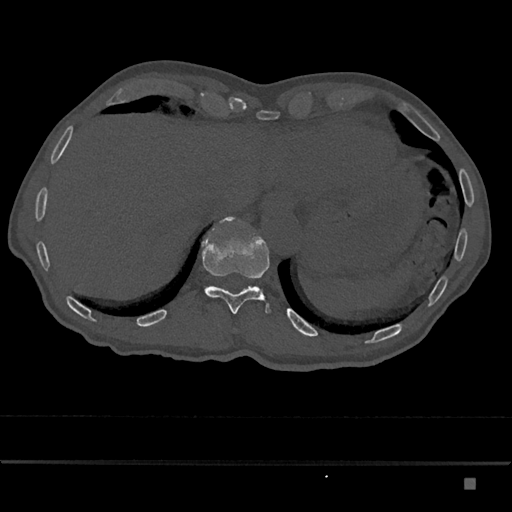
CT including the spine, one axial slice. Position 673 of 797 along the scan axis. Reconstruction kernel Br40s/3. 120 kVp. Bone window (W 1800 / L 400 HU). 512 × 512 image matrix, field of view 390 × 390 mm. Patient: male, 72 years. From the clinical record (not read from this slice): primary cancer: prostate.
Annotated regions visible in this slice (semi-automatically segmented with operator editing):
- T11 vertebra: bounding box (x1, y1, x2, y2) in pixels: (201, 216, 270, 314)